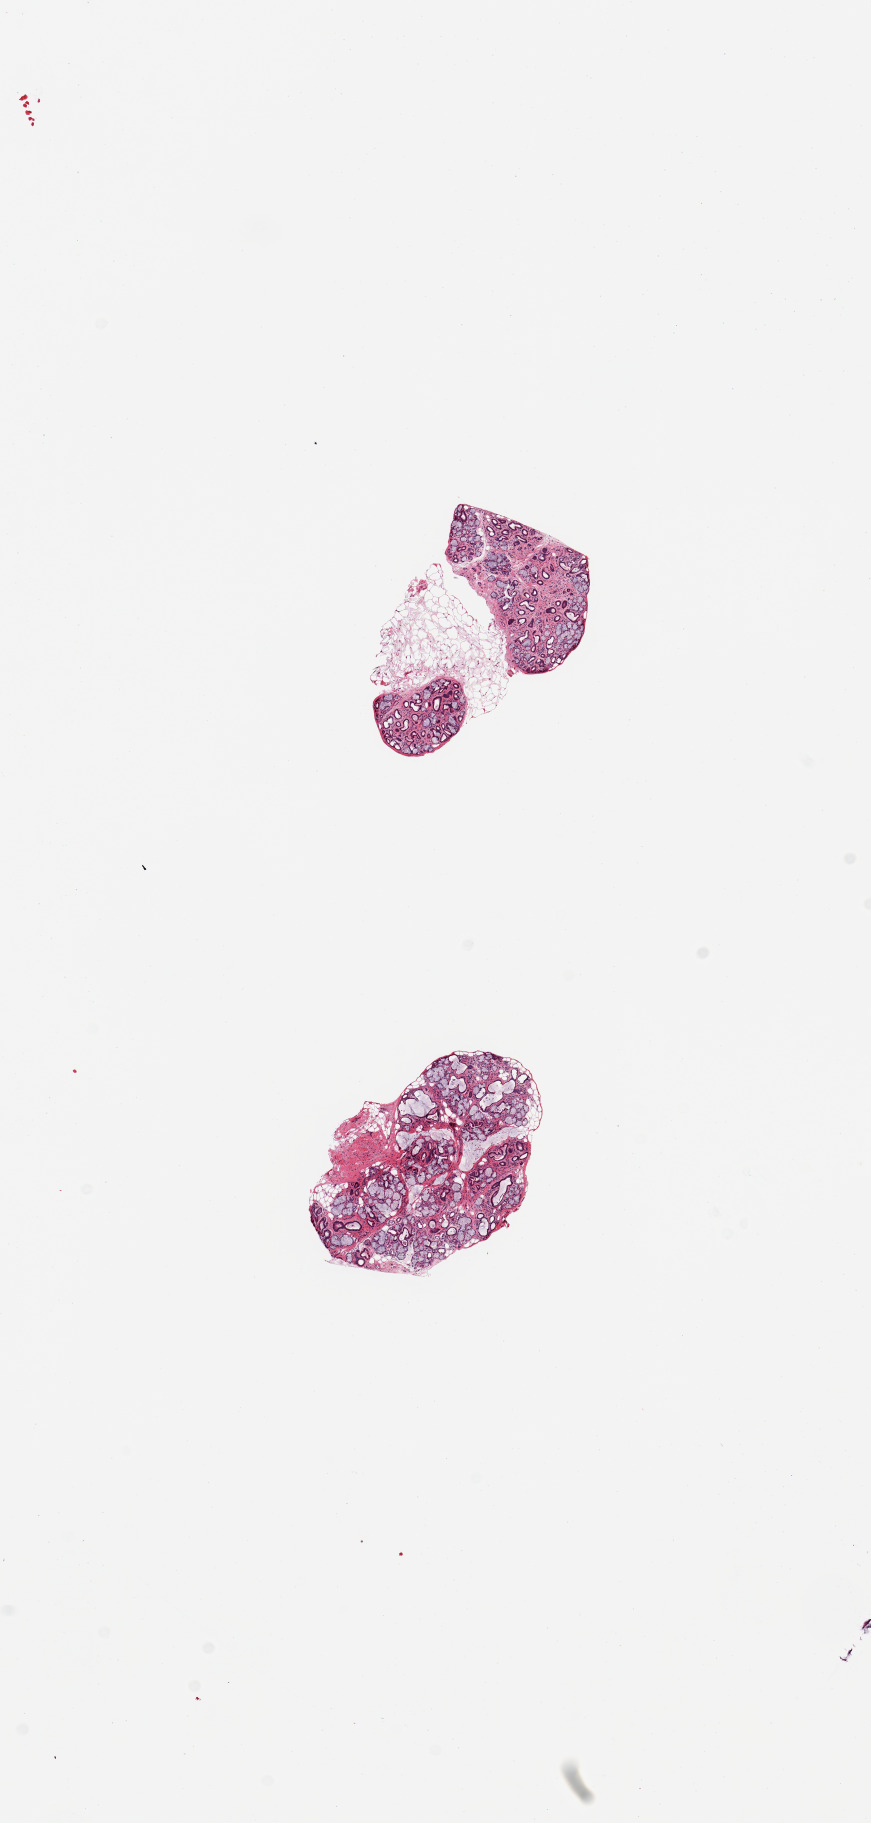
Digitized haematoxylin and eosin-stained section — whole scanned area (about 6.9 x 14.4 mm) shown as a low-resolution overview, PAXgene-fixed, paraffin-embedded tissue, sampled site (target tissue): minor salivary gland, donor tissue sample. Donor sex: female.
Review note (as recorded): 2 pieces, 70-80% target glandular tissue, good specimens.